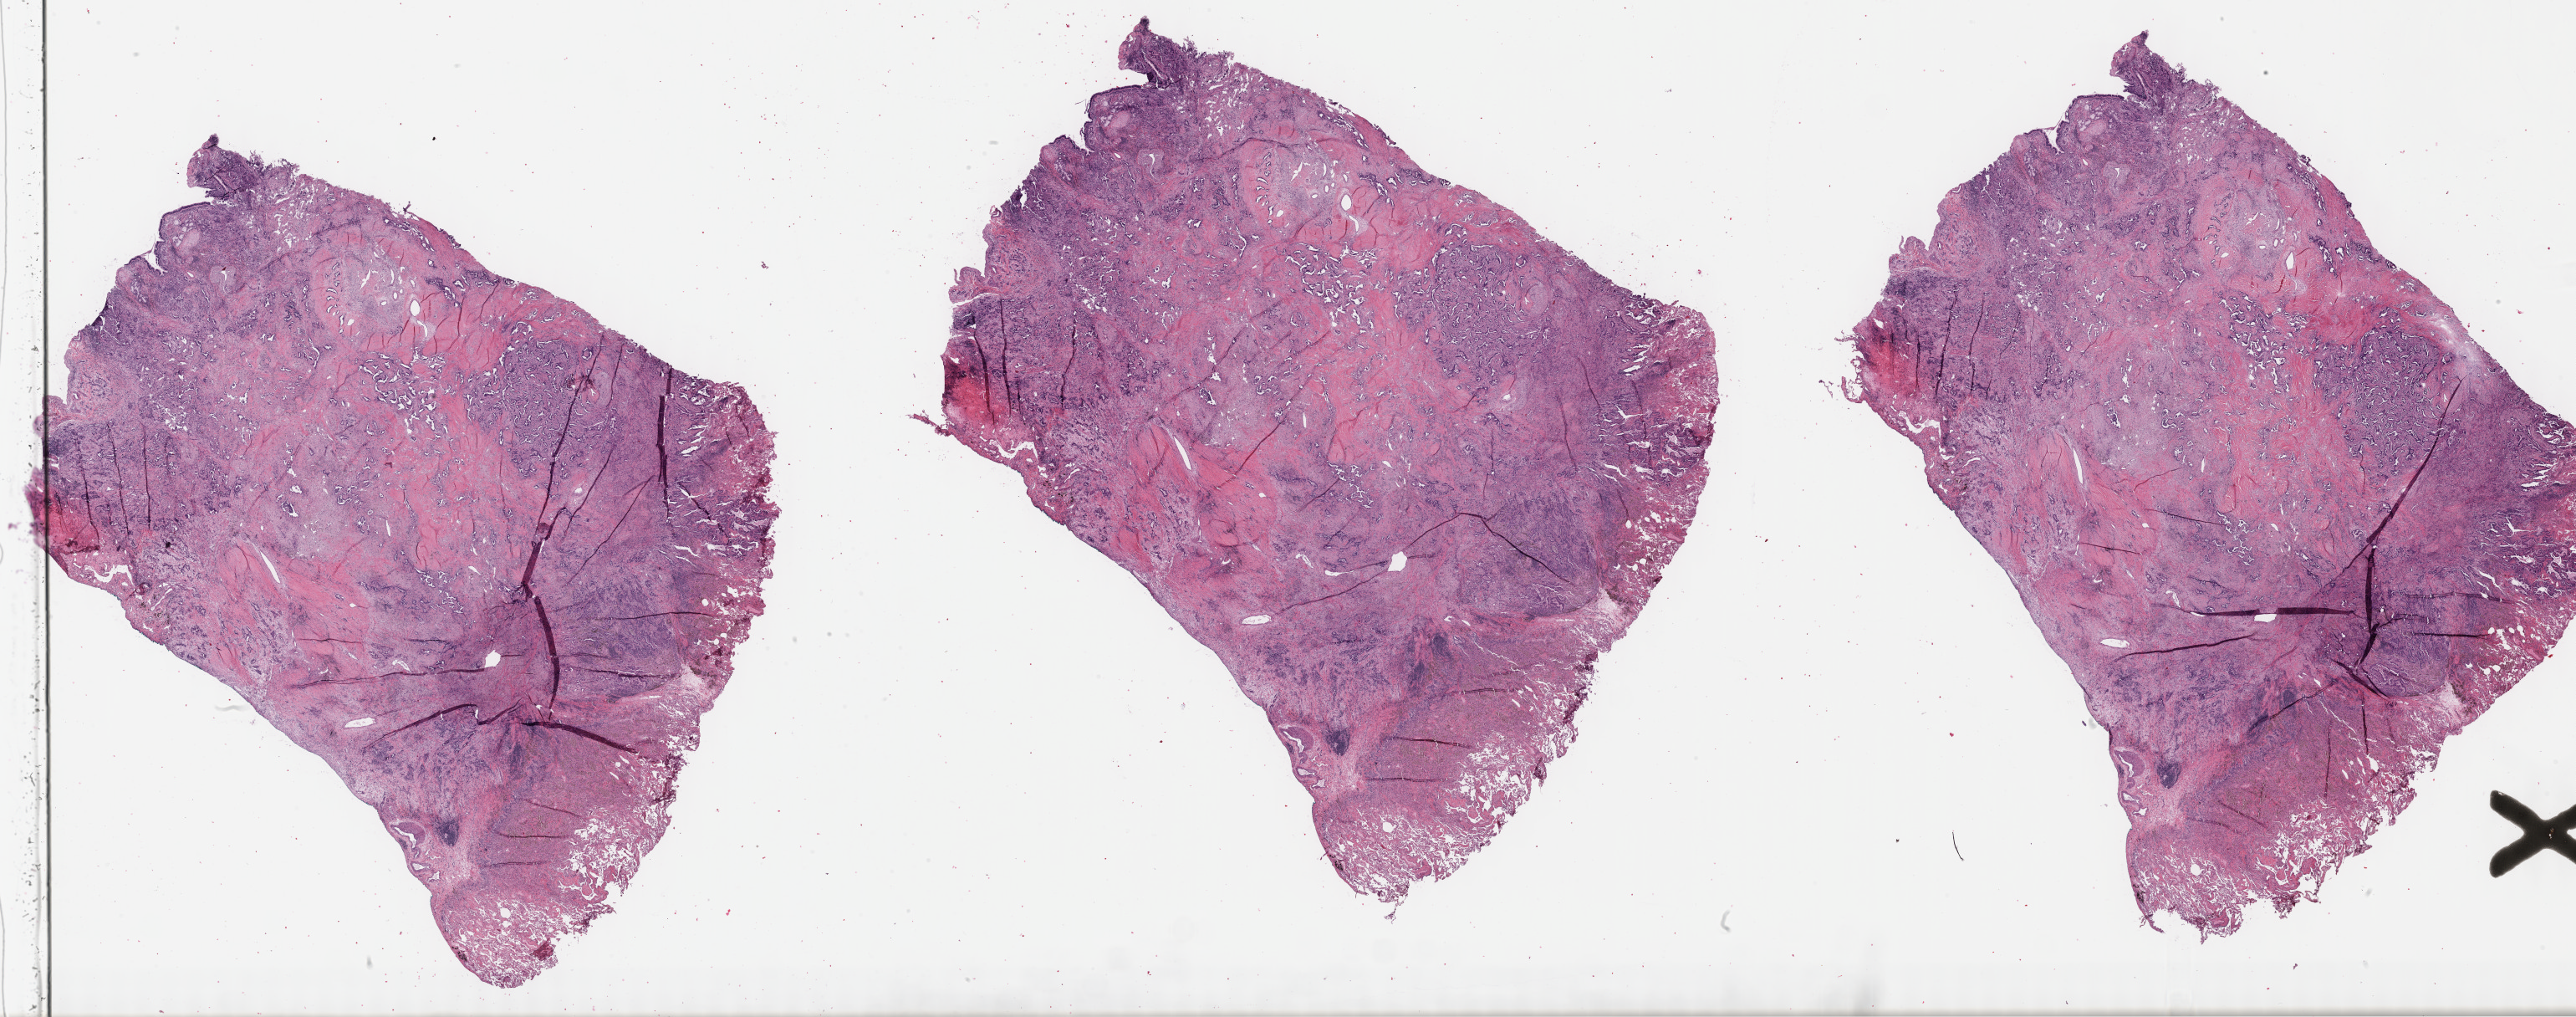
Digitized Hematoxylin and eosin (H&E) stained tissue section (whole slide), low-resolution overview of the scanned area, about 49.8 x 19.7 mm (acquisition: 40x scan); formalin-fixed paraffin-embedded (FFPE) diagnostic section; lung, primary tumour sample. Male patient; age at initial diagnosis 65 years.
Histologic diagnosis: Adenocarcinoma with mixed subtypes (upper lobe, lung). AJCC pathologic stage: IB (6th edition).